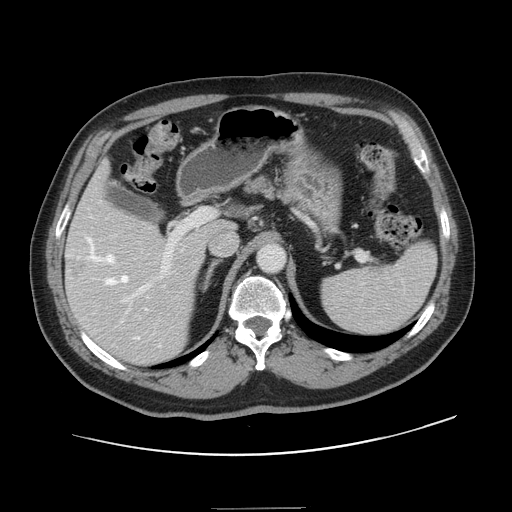
Contrast-enhanced abdominal CT, one axial slice; intravenous contrast given; soft-tissue window (W 400 / L 40 HU); 2.5 mm slice thickness; 512 × 512 image matrix, field of view 402 × 402 mm. Male patient, age 62 years. Case-level facts recorded for this patient, not image findings: diagnosis: colorectal cancer liver metastases, imaged before liver resection; multiple liver metastases: yes; largest metastasis: 2.7 cm.
Outlined on this slice (expert manual segmentation):
- hepatic veins: bounding box [x1, y1, x2, y2] px = [86, 237, 161, 346]
- liver: [66, 167, 233, 363]
- planned liver remnant (the part of the liver to remain after resection): [68, 168, 233, 247]
- portal vein (with intrahepatic branches): [78, 208, 213, 302]
- liver metastasis: [68, 259, 86, 277]